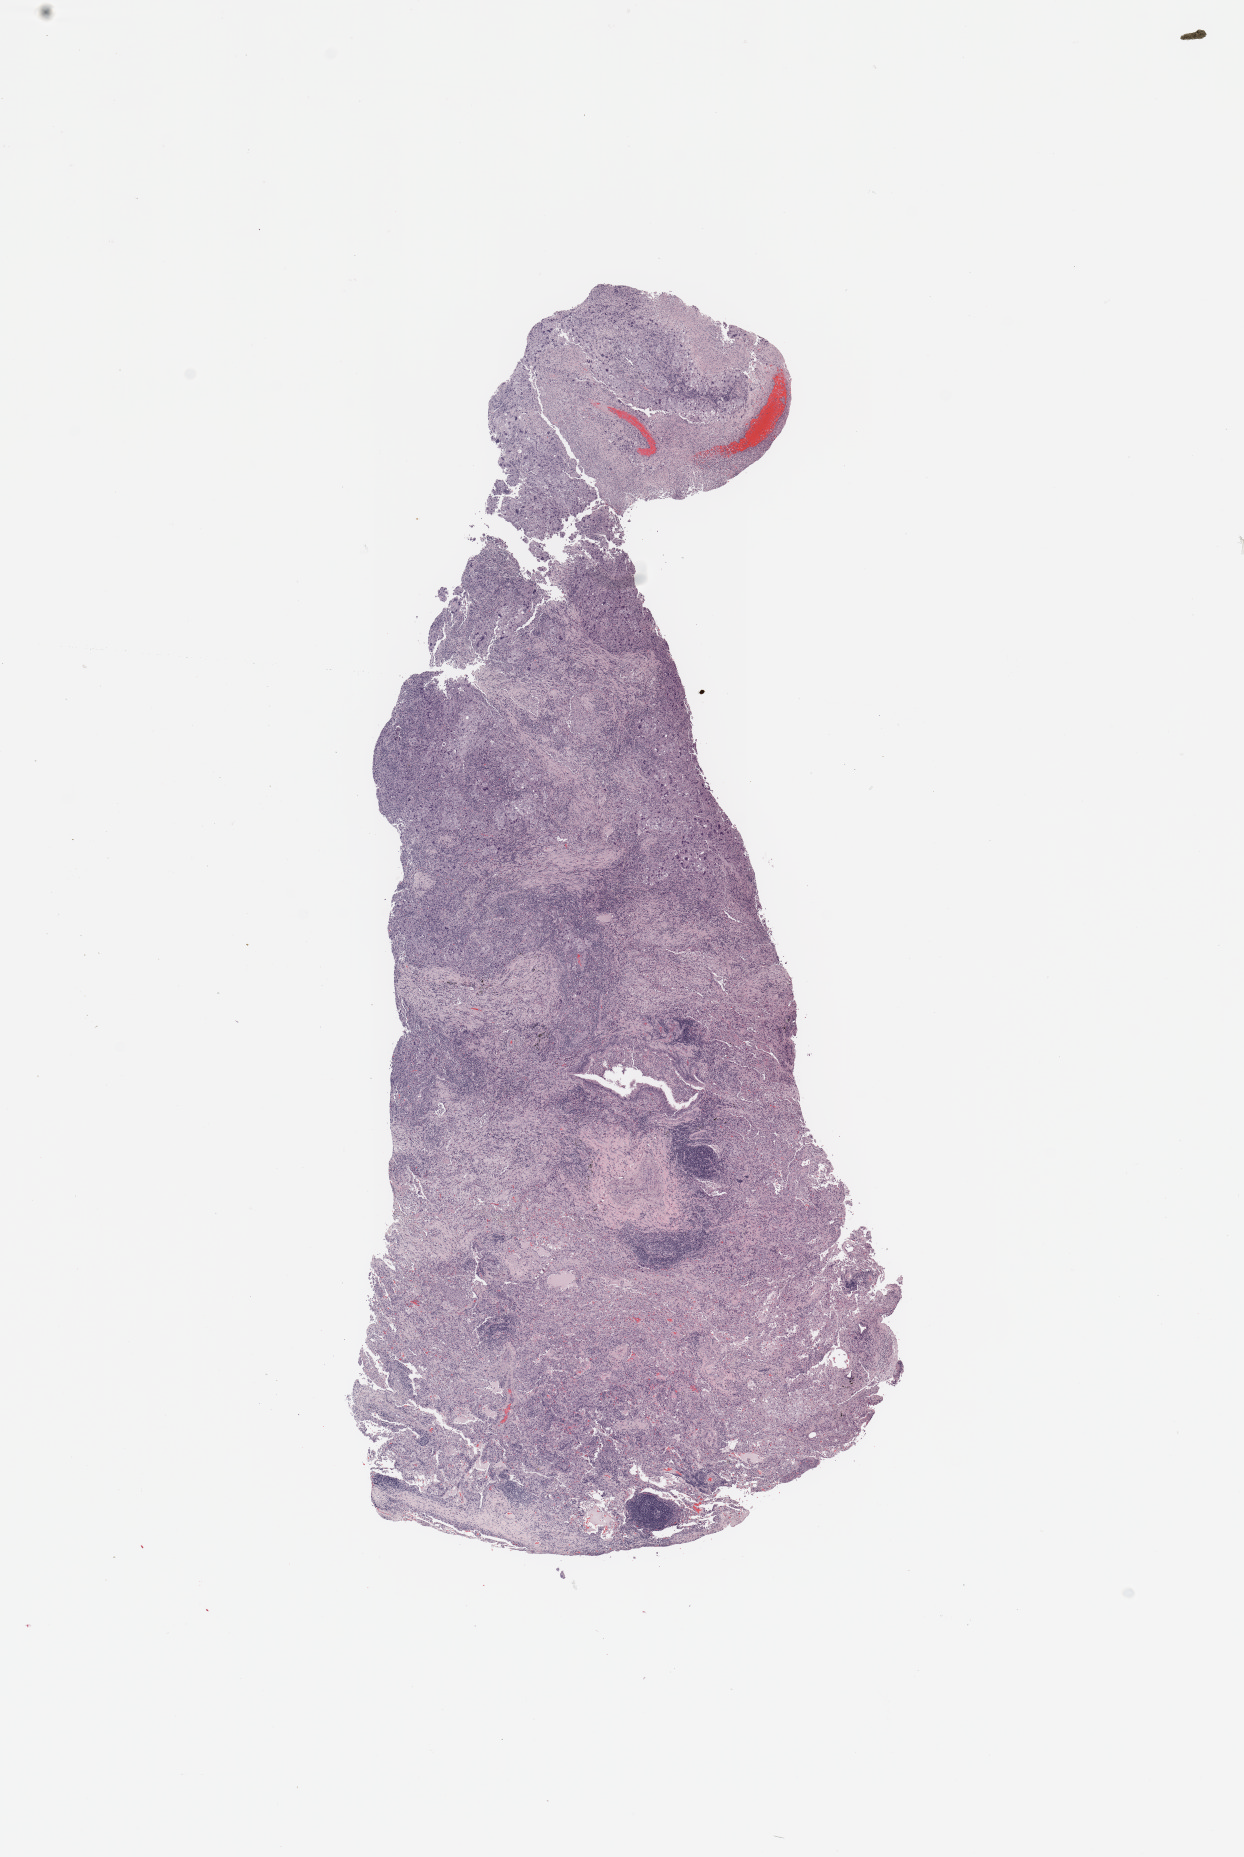
Digitized Hematoxylin and eosin (H&E) stained tissue section (whole slide), low-resolution overview of the scanned area, about 9.8 x 14.7 mm (acquisition: 20x scan), tumour tissue sample, lung. 66-year-old female patient. Histologic grade: G3 (poorly differentiated).
• diagnosis: Adenocarcinoma, NOS
• AJCC pathologic stage: IIA